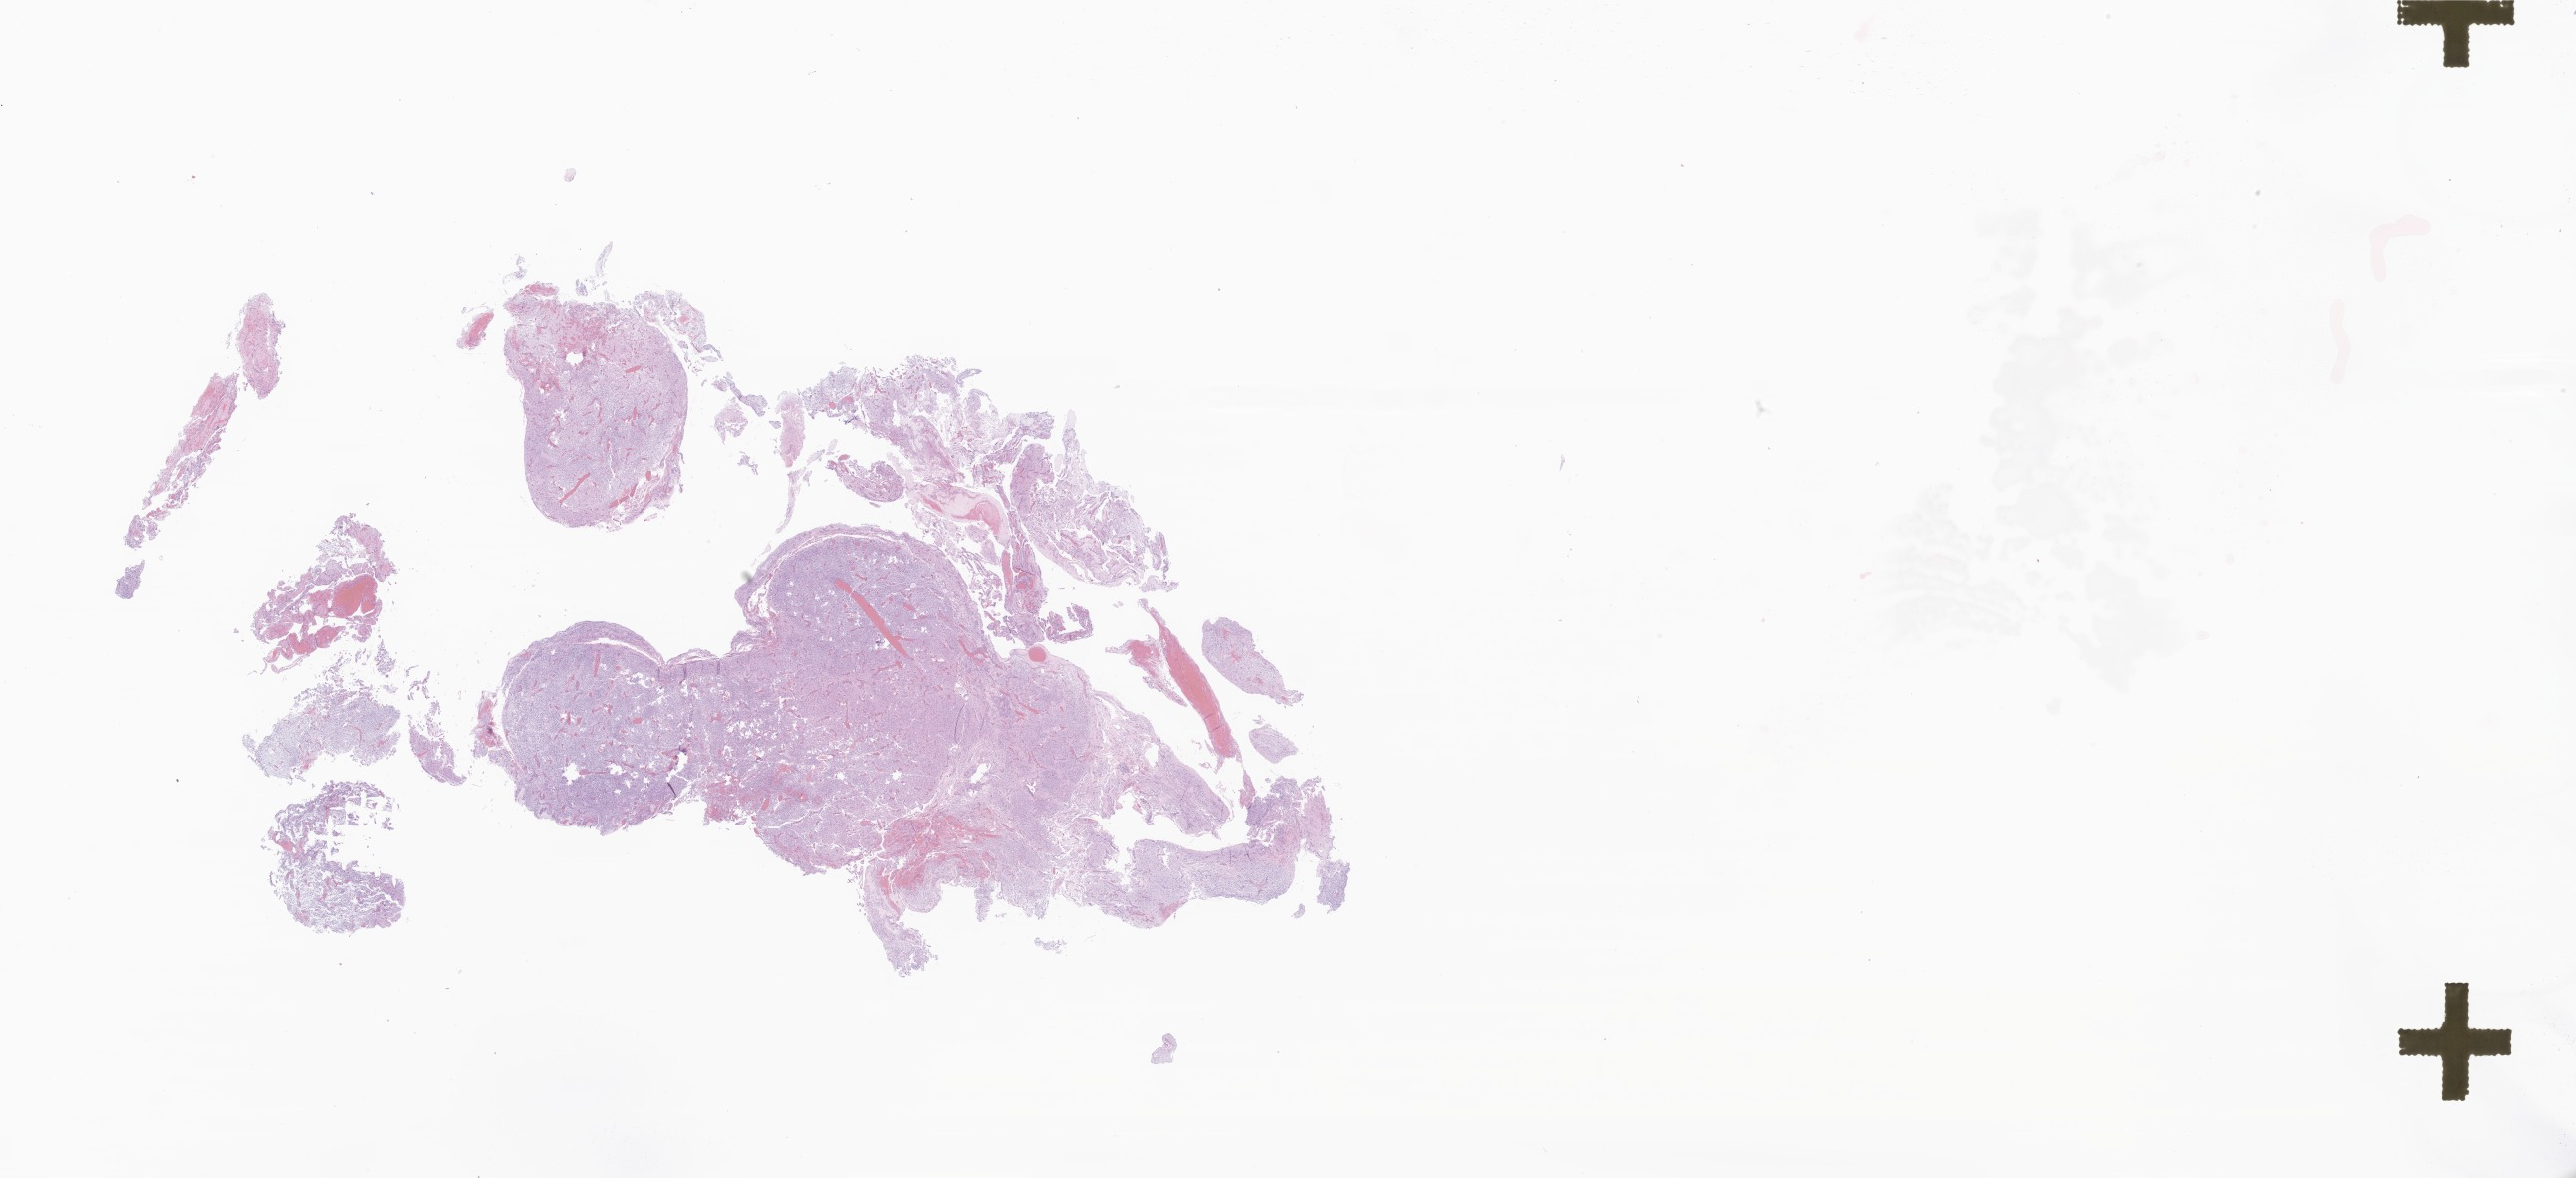
Whole-slide image, hematoxylin and eosin (H&E) stain of tumor tissue from the frontal lobe — whole scanned area (about 43.6 x 20.0 mm) shown as a low-resolution overview; FFPE section. Patient: female, age 129 months (10 years 9 months).
Recorded diagnosis: Ganglioglioma, NOS.